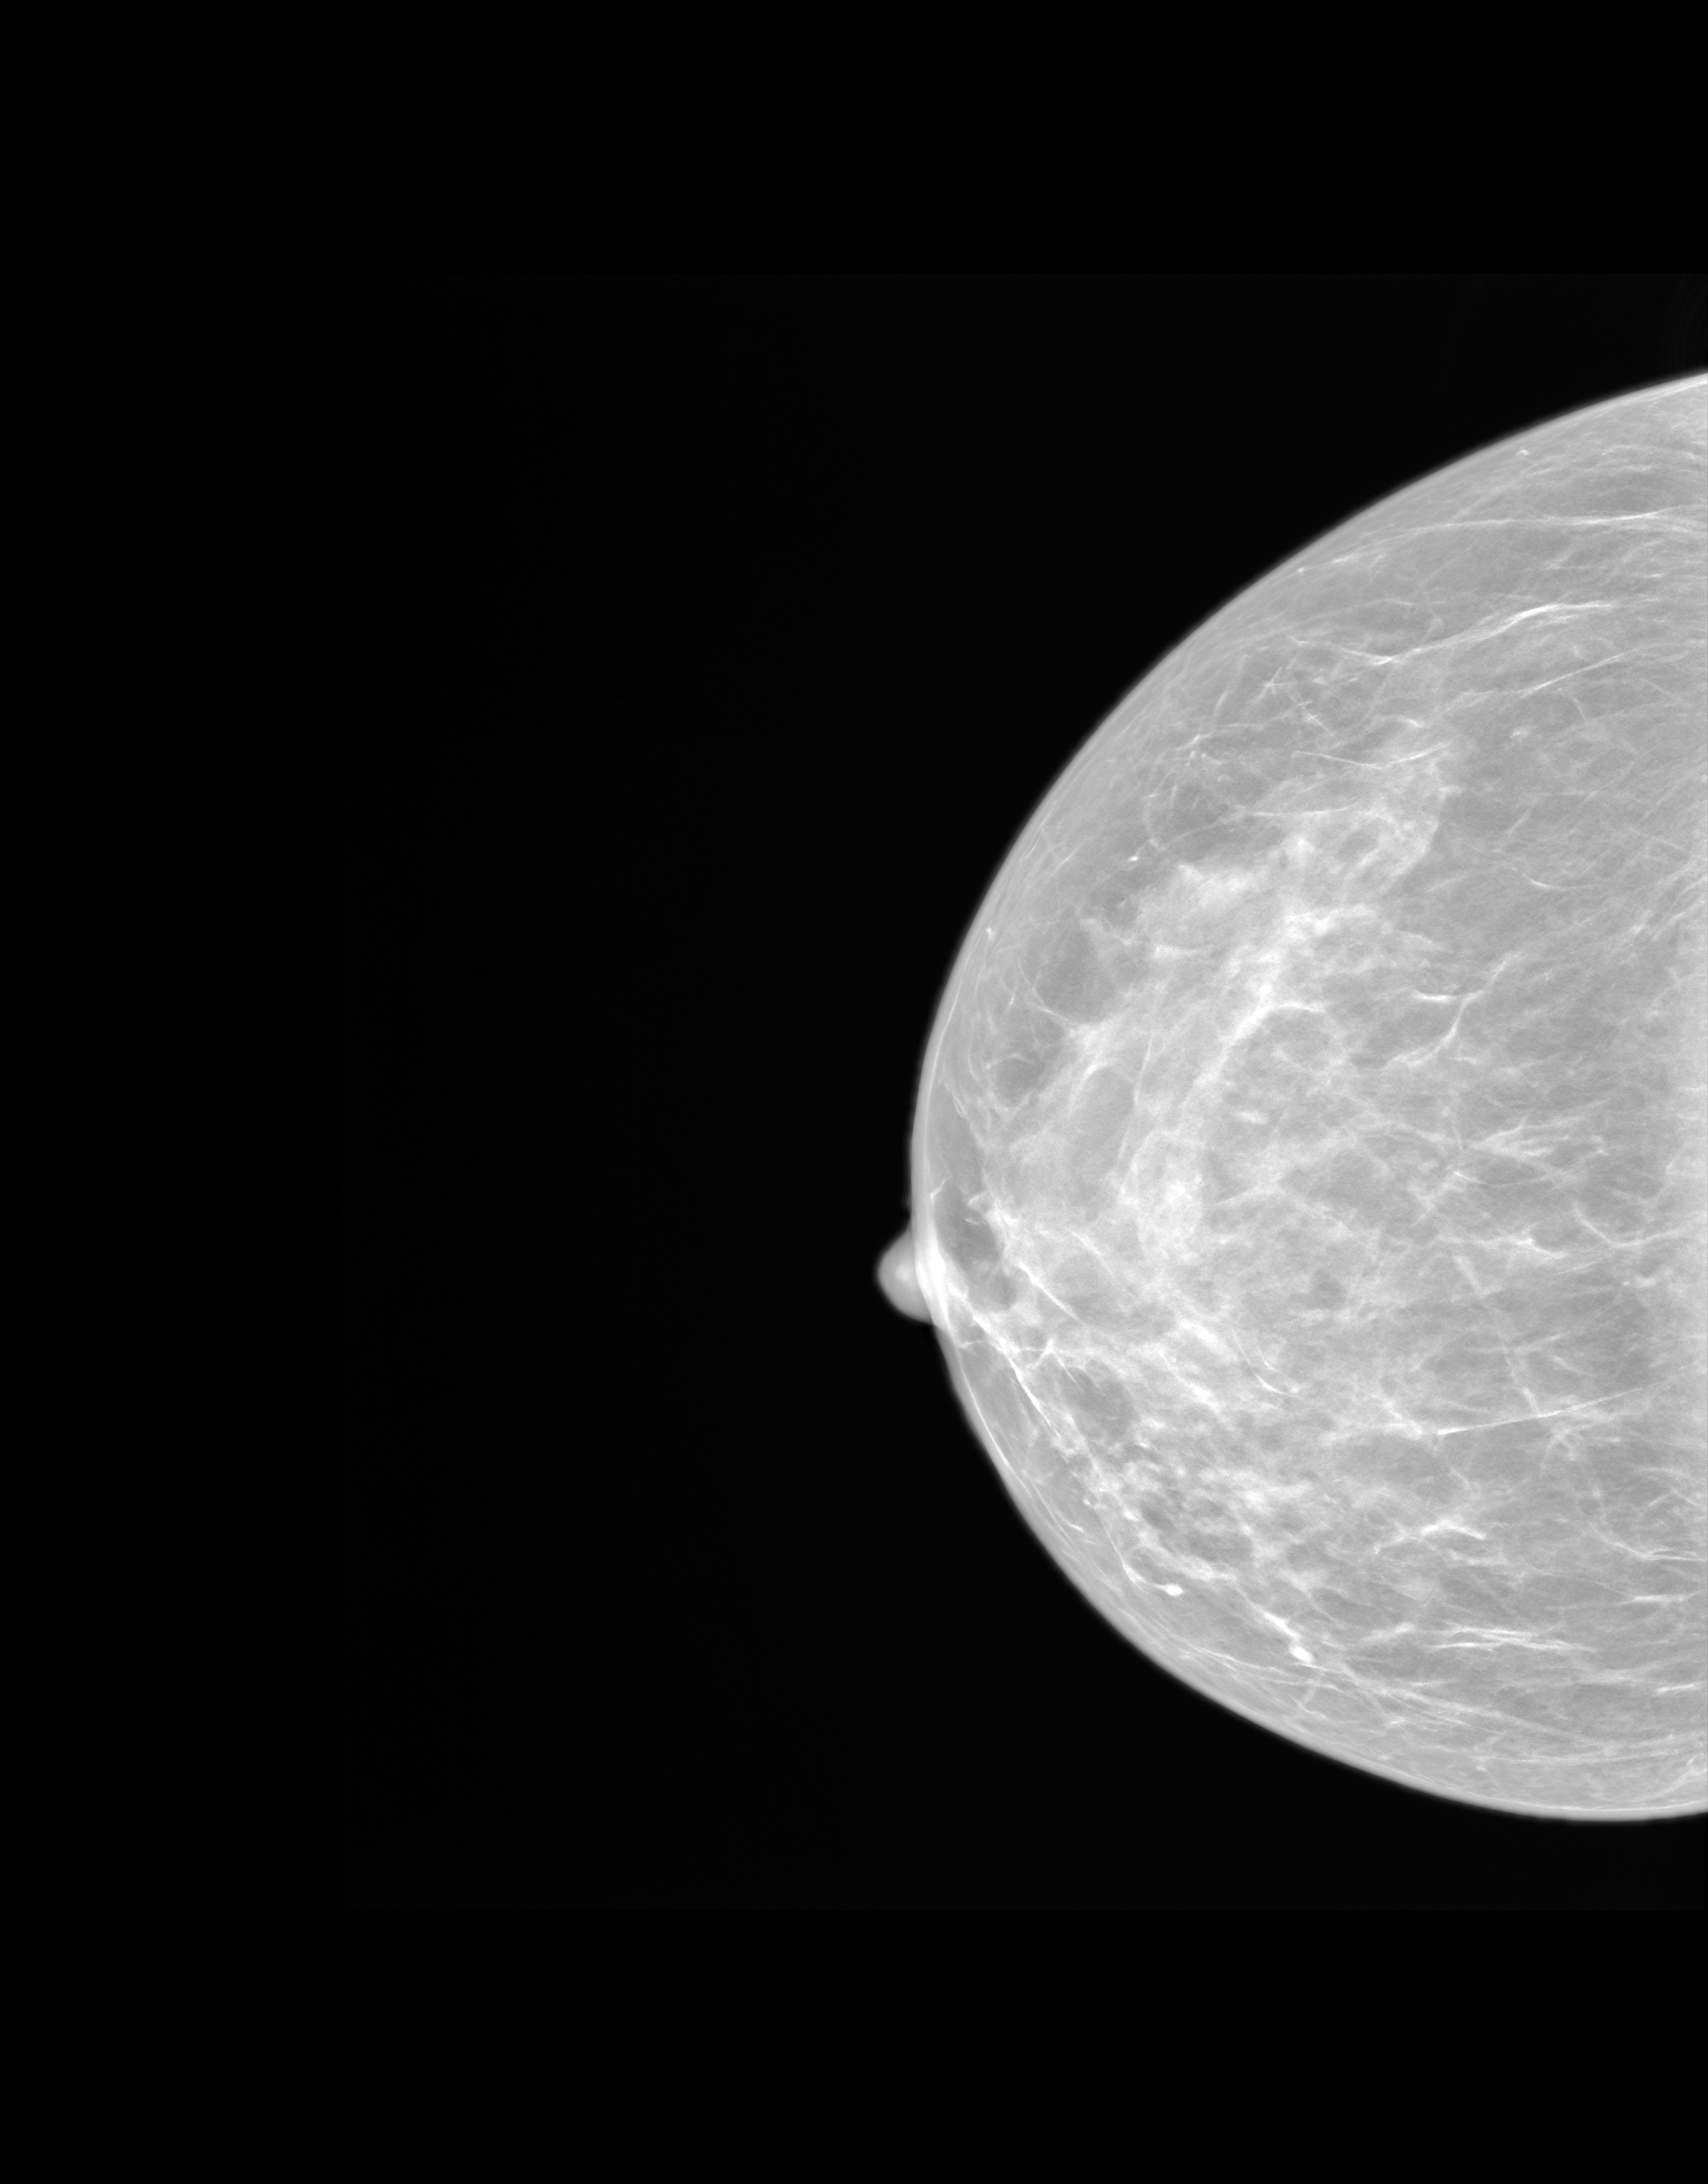
Synthetic 2-D view generated from a tomosynthesis acquisition (not an FFDM exposure); right breast; CC view; screening examination. Patient aged 53 years (female).
BI-RADS breast density category at the screening exam (both breasts, scale 1–4): 3. Final BI-RADS assessment for this screening round (tomosynthesis exam, both breasts): category 1. Recall: no recall after this screen.